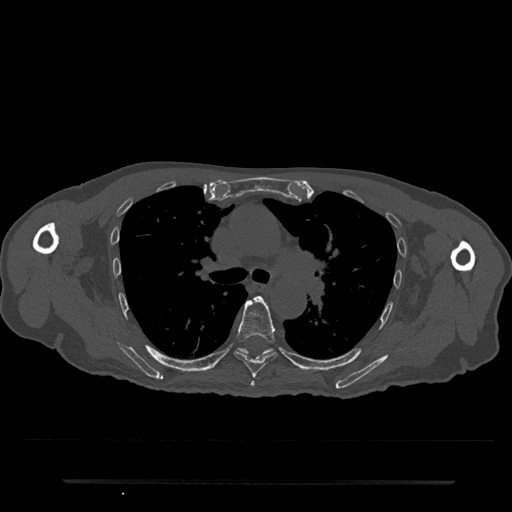
CT including the spine, one axial slice; position 522 of 797 along the scan axis; 120 kVp; bone window (W 1800 / L 400 HU); 512 × 512 image matrix, field of view 427 × 427 mm. Male patient, age 74 years. Case-level facts recorded for this patient, not image findings: primary cancer: prostate.
Annotated regions visible in this slice (semi-automatically segmented with operator editing):
- T5 vertebra: box from (x=250, y=381) to (x=255, y=386) px
- T6 vertebra: (x=234, y=296)–(x=277, y=379)
- T7 vertebra: (x=238, y=348)–(x=273, y=359)